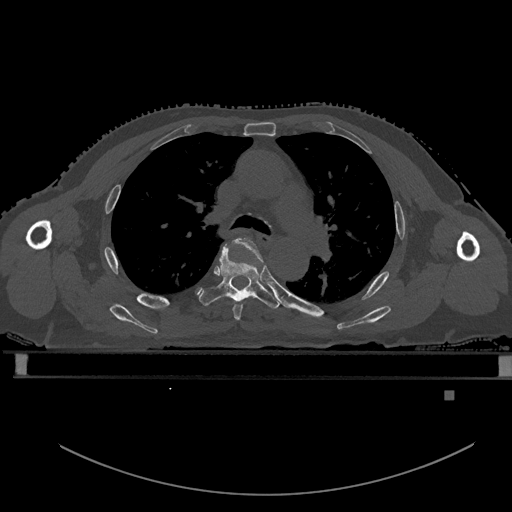
CT including the spine, one axial slice; position 372 of 969 along the scan axis; bone window (W 1800 / L 400 HU); 0.5 mm slice thickness; 512 × 512 image matrix. Patient: male, 82 years. Case-level facts recorded for this patient, not image findings: primary cancer: prostate; vertebrae with lytic lesions (as recorded): T11, T9, T8, T2.
Annotated regions visible in this slice (semi-automatically segmented with operator editing):
- T4 vertebra: box from (x=233, y=238) to (x=262, y=321) px
- T5 vertebra: (x=200, y=245)–(x=280, y=309)